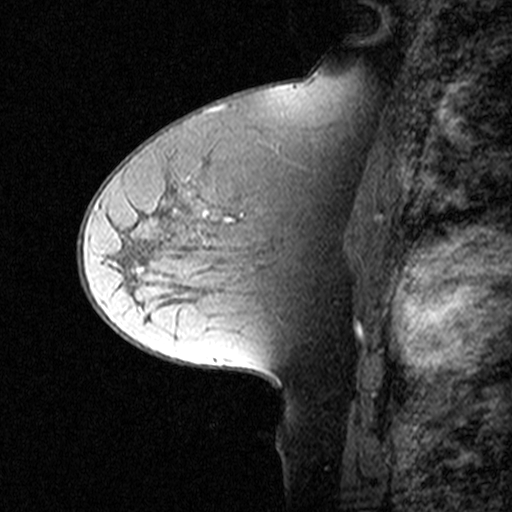
Breast MRI (dynamic contrast-enhanced), one sagittal slice; position 28 of 44 along the scan axis; dynamic contrast-enhanced study with each time point stored as its own series, time point 2 of 3 at this slice position (early post-contrast, ordered by acquisition time); 1.5 T; TE 4.5 ms, TR 11 ms; 3 mm slice thickness; 512 × 512 image matrix. Female patient, age 50 years. Case-level facts recorded for this patient, not image findings: setting: breast cancer imaged before/during neoadjuvant chemotherapy; receptor status: HR-positive, HER2-negative.
Annotated regions visible in this slice (semi-automatically segmented with operator editing):
- analysis volume of interest (the breast-tissue region the enhancement analysis was run in; not a lesion): bounding box [x1, y1, x2, y2] px = [126, 162, 329, 291]
- tumour enhancement mask (voxels above the 90 % enhancement threshold inside the analysis volume of interest): [214, 217, 232, 220]